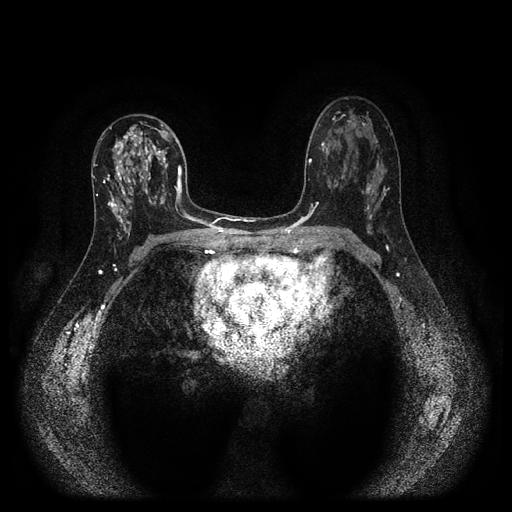
Breast MRI (dynamic contrast-enhanced, multi-phase), one axial slice. Position 59 of 116 along the scan axis. Dynamic contrast-enhanced series, time point 2 of 5 at this slice position (early post-contrast). 1.5 T. TE 2.7 ms, TR 5.4 ms. 2 mm slice thickness. 512 × 512 image matrix. Female patient, age 47 years.
Annotated regions visible in this slice (semi-automatic segmentation, software-assisted and operator-edited):
- breast lesion (labelled 'tumour' in the annotation; benign lesions carry a separate 'benign' label): bounding box [x1, y1, x2, y2] px = [112, 124, 170, 222]